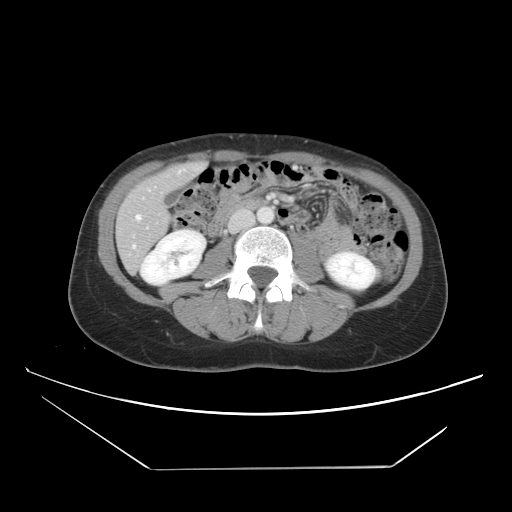
Contrast-enhanced abdominal CT, one axial slice; 120 kVp; intravenous contrast given; soft-tissue window (W 400 / L 40 HU); 5 mm slice thickness; 512 × 512 image matrix, field of view 399 × 399 mm. Female patient, age 52 years. From the clinical record (not read from this slice): diagnosis: colorectal cancer liver metastases, imaged before liver resection; multiple liver metastases: yes; largest metastasis: 5.5 cm; disease in both lobes: yes.
Annotated regions visible in this slice (manually delineated by an expert):
- hepatic veins: bounding box [x1, y1, x2, y2] px = [133, 166, 202, 248]
- liver: [118, 164, 202, 269]
- planned liver remnant (the part of the liver to remain after resection): [124, 164, 202, 217]
- portal vein (with intrahepatic branches): [267, 196, 270, 199]